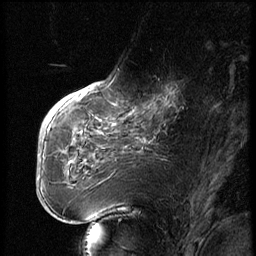
Breast MRI (dynamic contrast-enhanced), one sagittal slice; slice 24 of 74 in the series (ordered by position); dynamic contrast-enhanced series, image 2 of 3 at this slice position (ordered by acquisition); 1.5 T; TE 4.2 ms, TR 9 ms; 256 × 256 image matrix. Female patient, age 56 years. Case-level facts recorded for this patient, not image findings: setting: breast cancer imaged before/during neoadjuvant chemotherapy.
Outlined on this slice (semi-automatic segmentation, software-assisted and operator-edited):
- analysis volume of interest (the breast-tissue region the enhancement analysis was run in; not a lesion): bounding box <123,71,195,131> (left, top, right, bottom; pixels)
- tumour enhancement mask (voxels above the 140 % enhancement threshold inside the analysis volume of interest): <133,87,176,115>